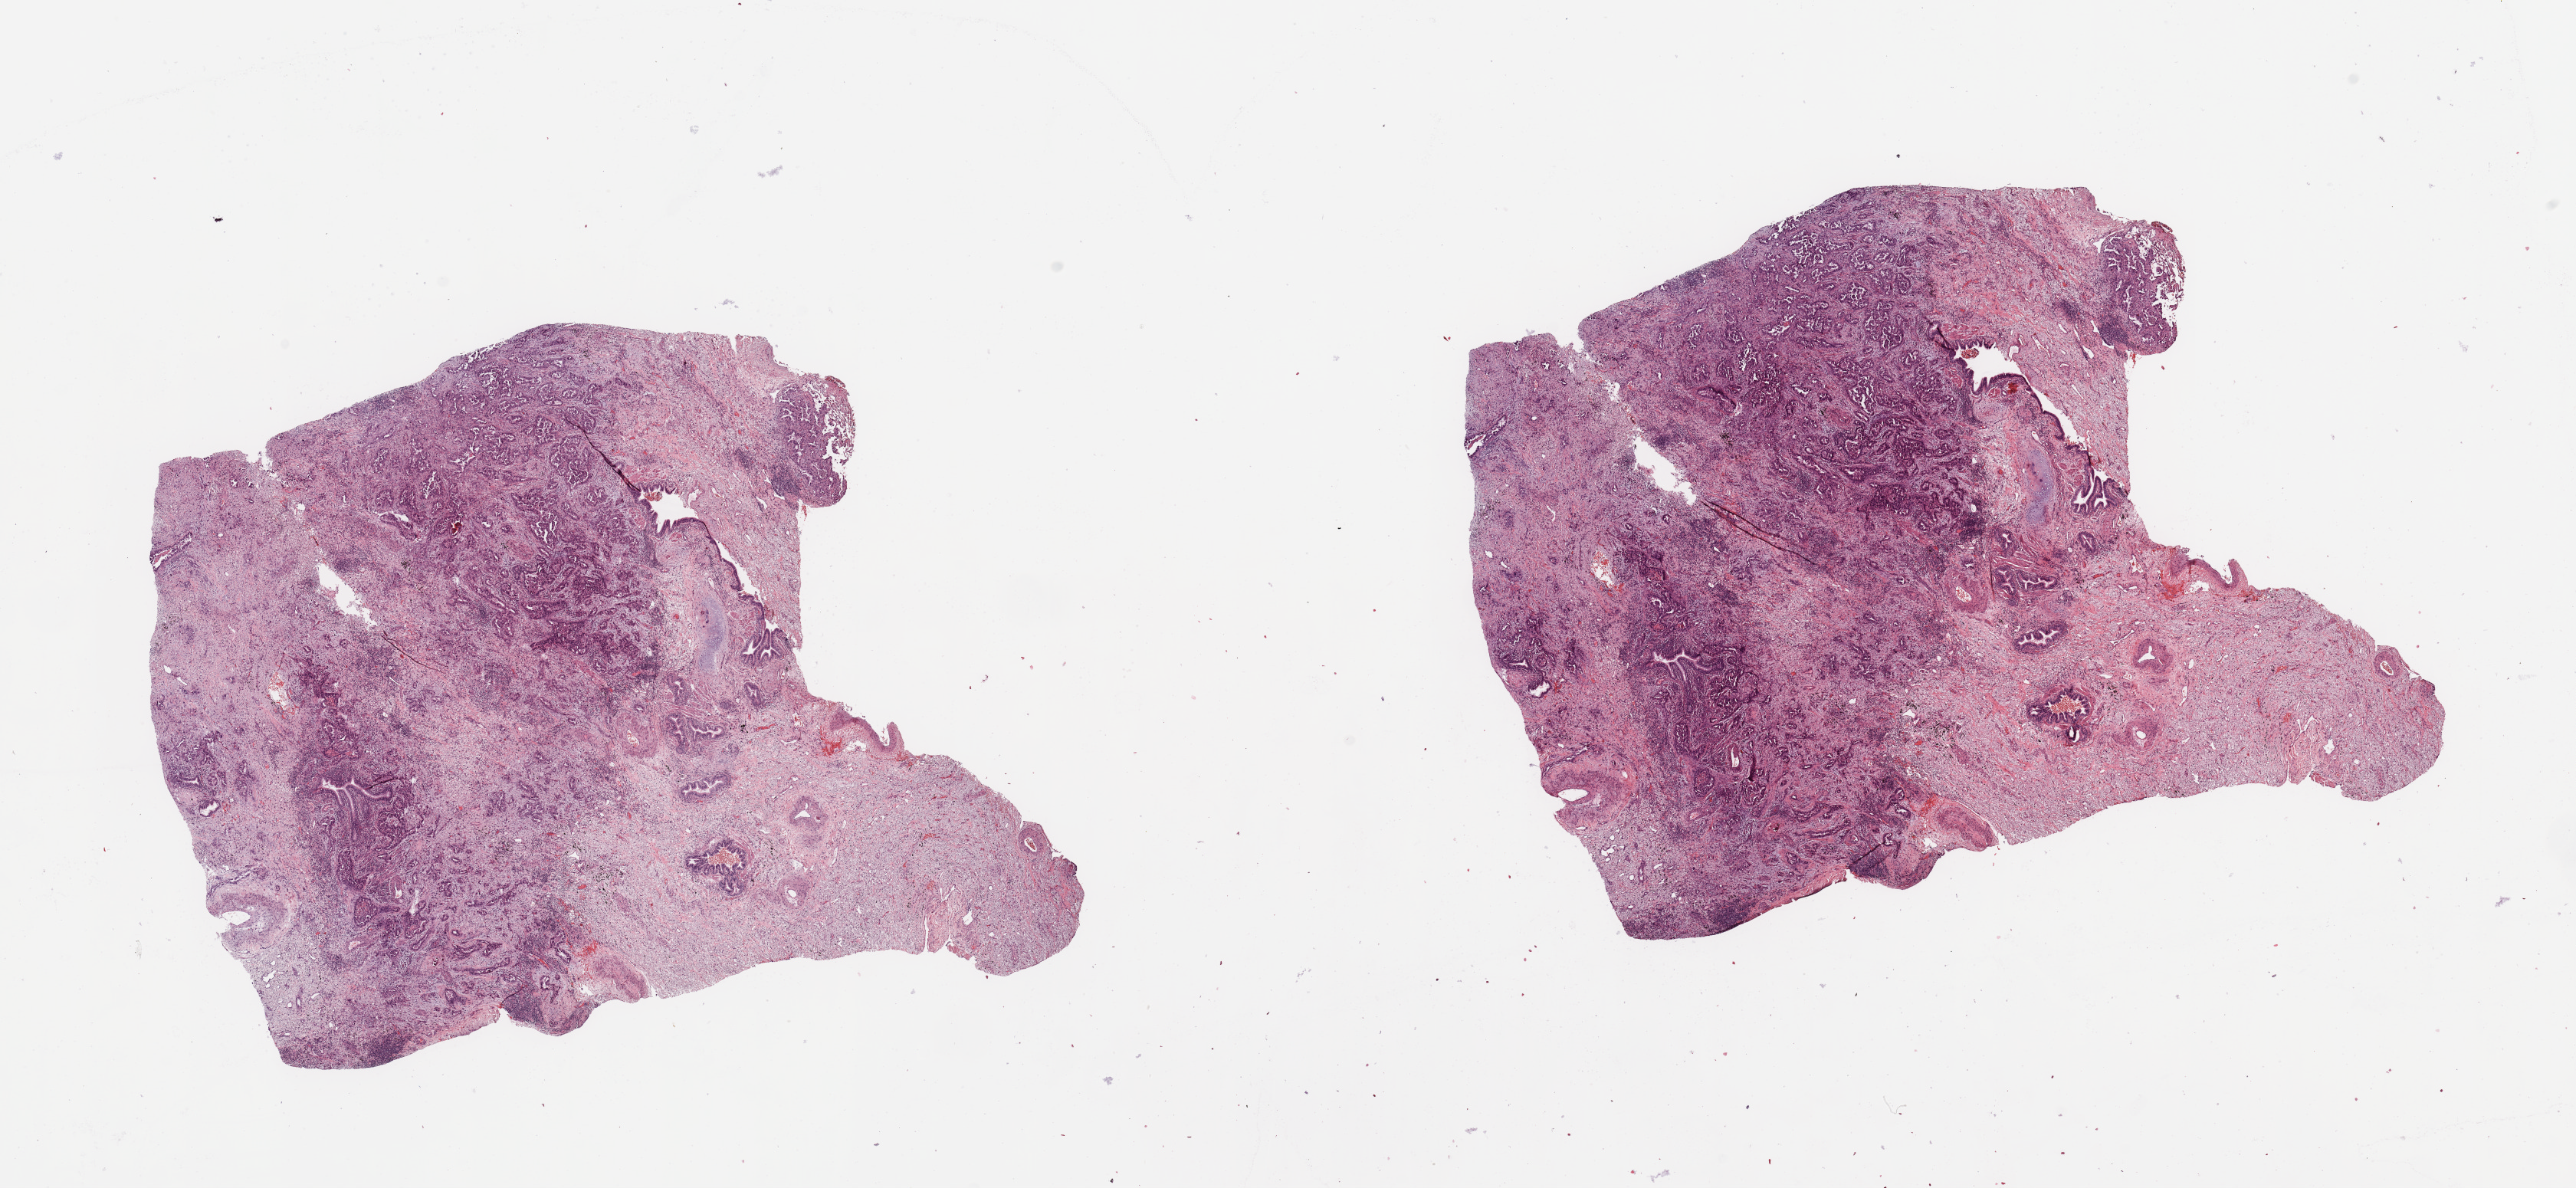
Whole-slide histology image, H&E — low-resolution overview of the scanned area, about 26.6 x 12.3 mm (slide scanned at 20x), lung, tumour tissue. Patient: female, age 67 years. Histologic grade: G2 (moderately differentiated).
* AJCC pathologic stage: II
* diagnosis: Adenocarcinoma, NOS